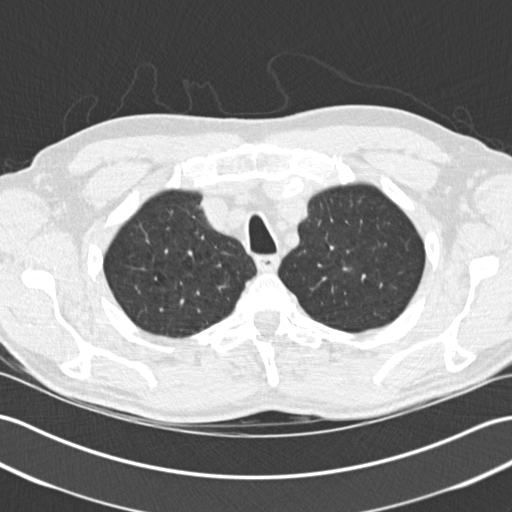
Low-dose screening chest CT, axial slice. First (baseline) screen. Lung window (W 1500 / L -600 HU). Standard (soft-tissue) reconstruction kernel (B30f). 512 × 512 image matrix. Male participant, aged 64 years at enrolment. Former smoker at enrolment.
- Expert-annotated lung lesion, bounding box (x1, y1, x2, y2) in pixels: (328, 253, 366, 285).
- Screening reader's record for this exam (one nodule recorded; not confirmed to be the boxed lesion): non-calcified nodule or mass ≥4 mm, right upper lobe, 7 × 5 mm, spiculated (stellate) margins, soft tissue attenuation.
- Note: the box lies in the patient's left hemithorax on this image, whereas the reader's record names the right lung; they may be different findings.